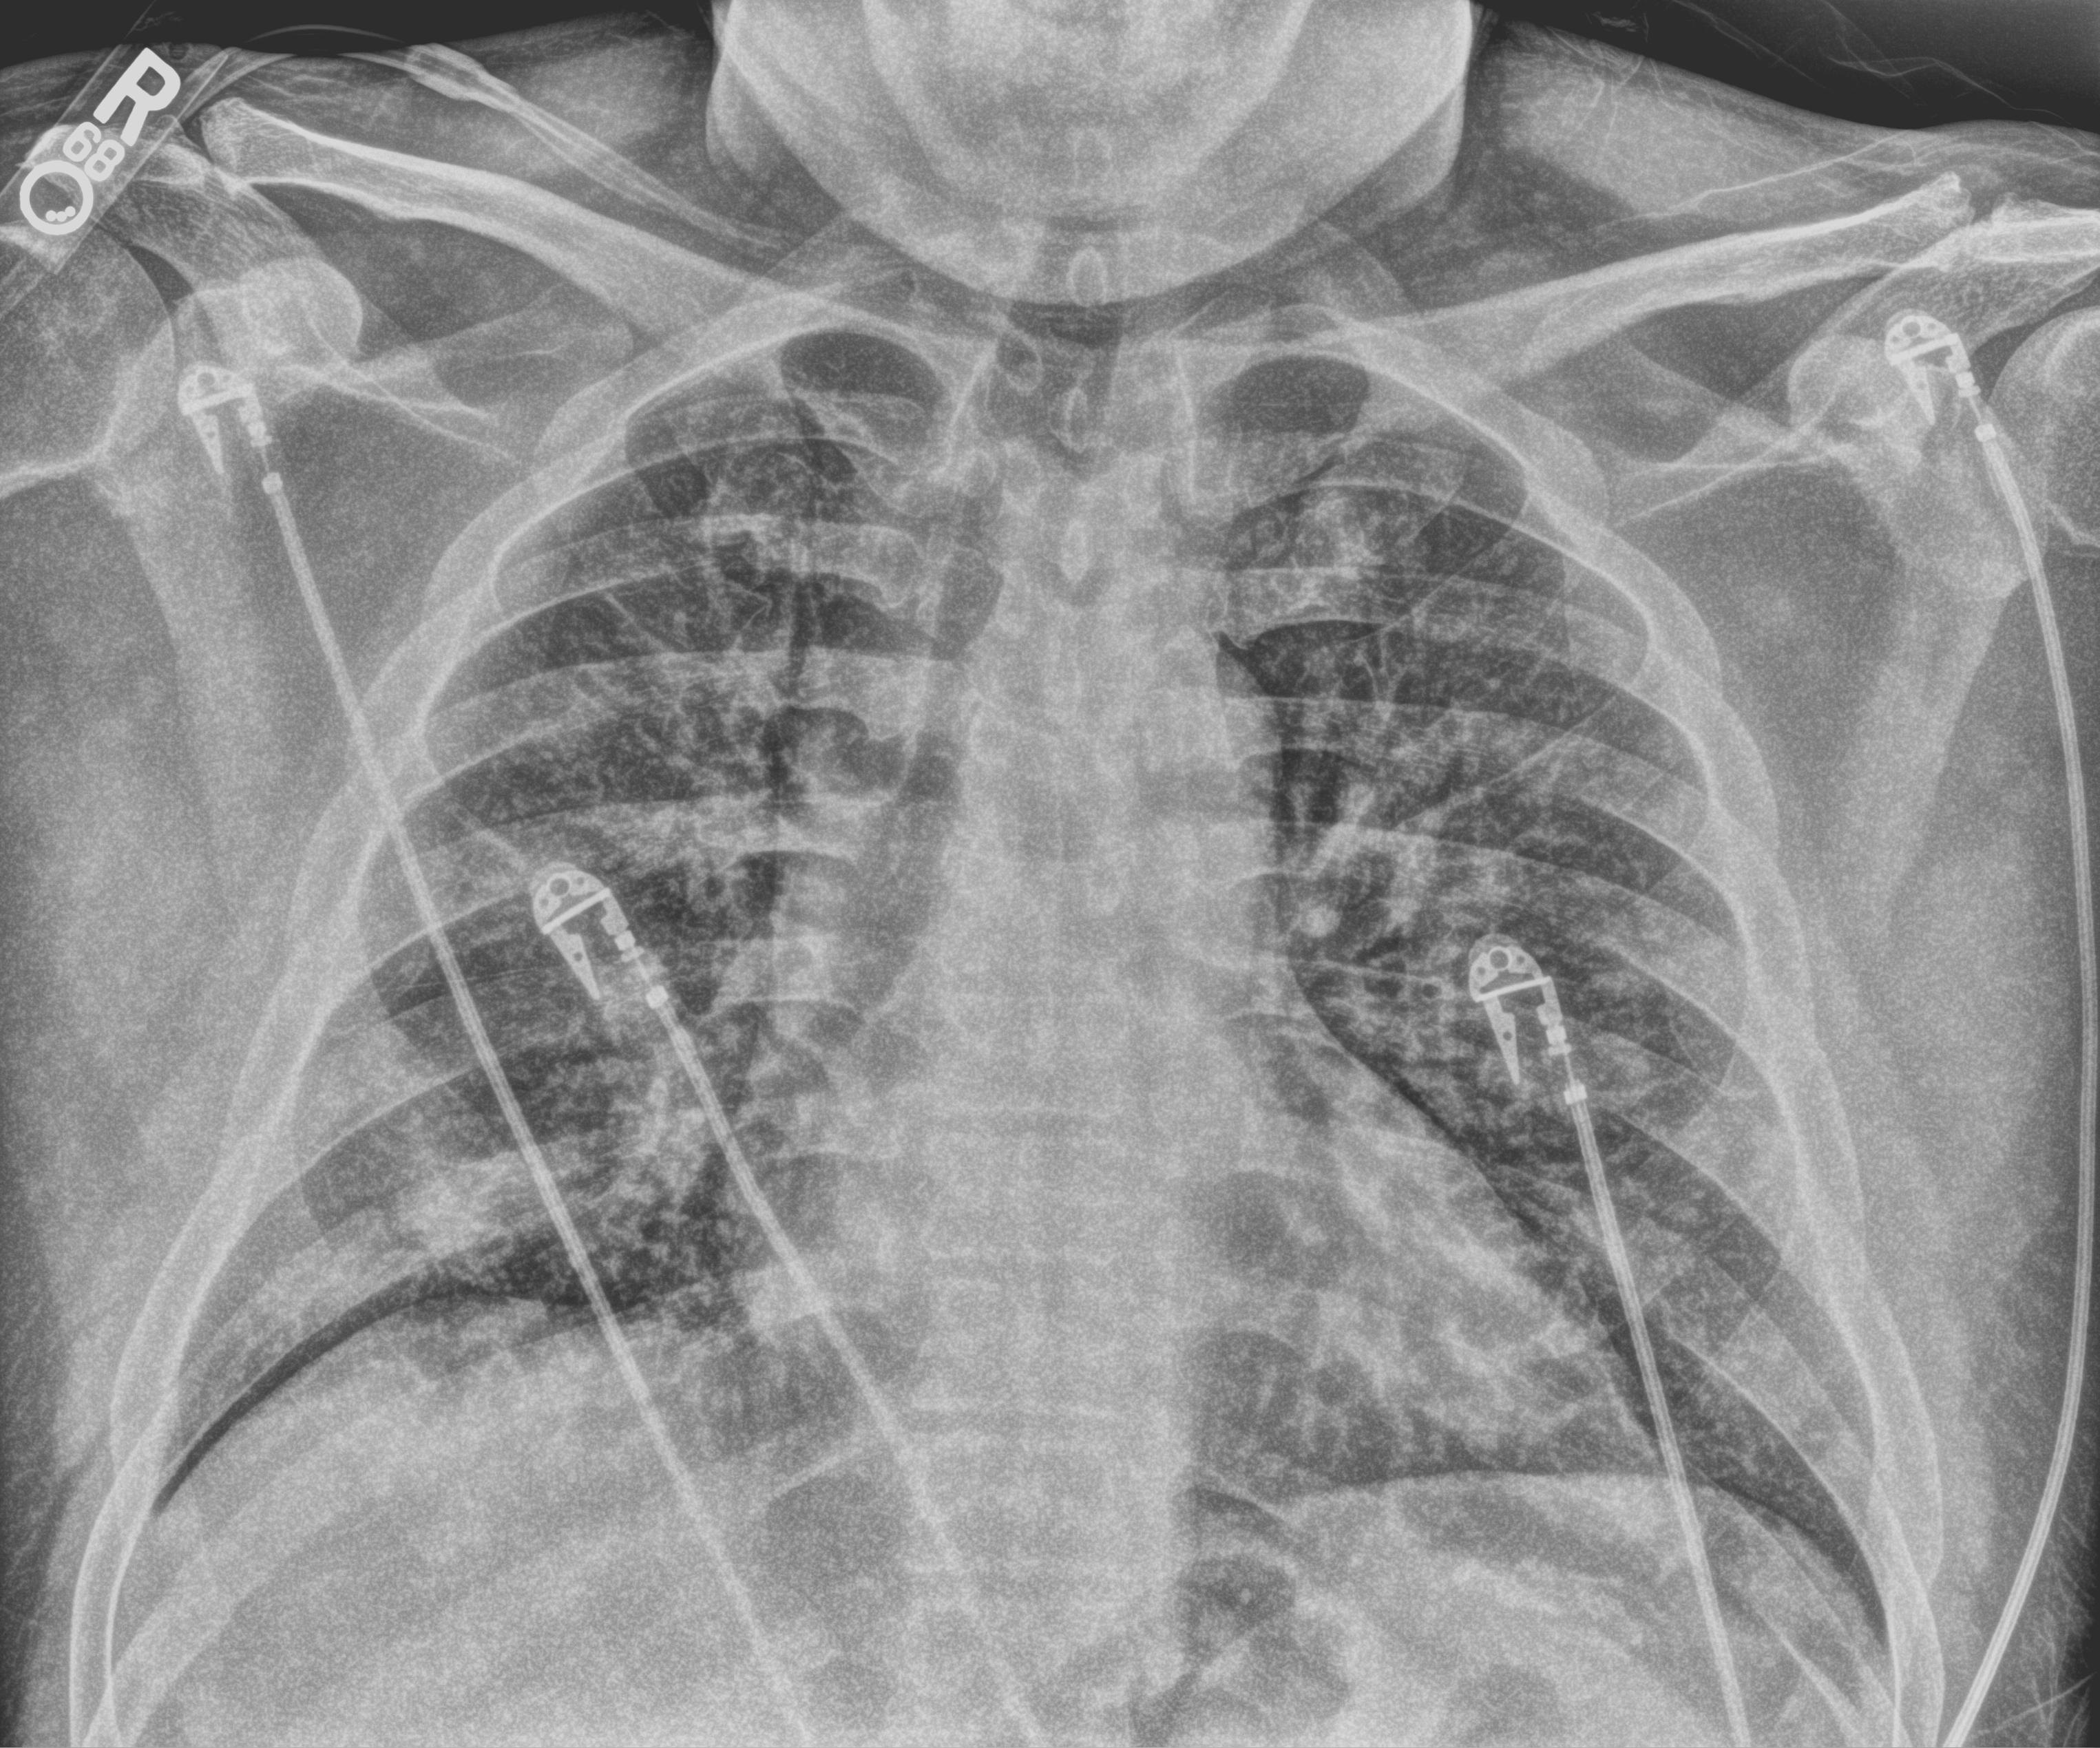
Chest X-ray (portable), anteroposterior (AP) projection. Patient hospitalised with COVID-19; male, aged 18–59 years.
Hospital-stay facts (about this admission, not read from this image; timing relative to this image not recorded):
- mechanically ventilated during this hospital stay: no
- length of hospital stay: 8 days
- admitted to intensive care during this hospital stay: no